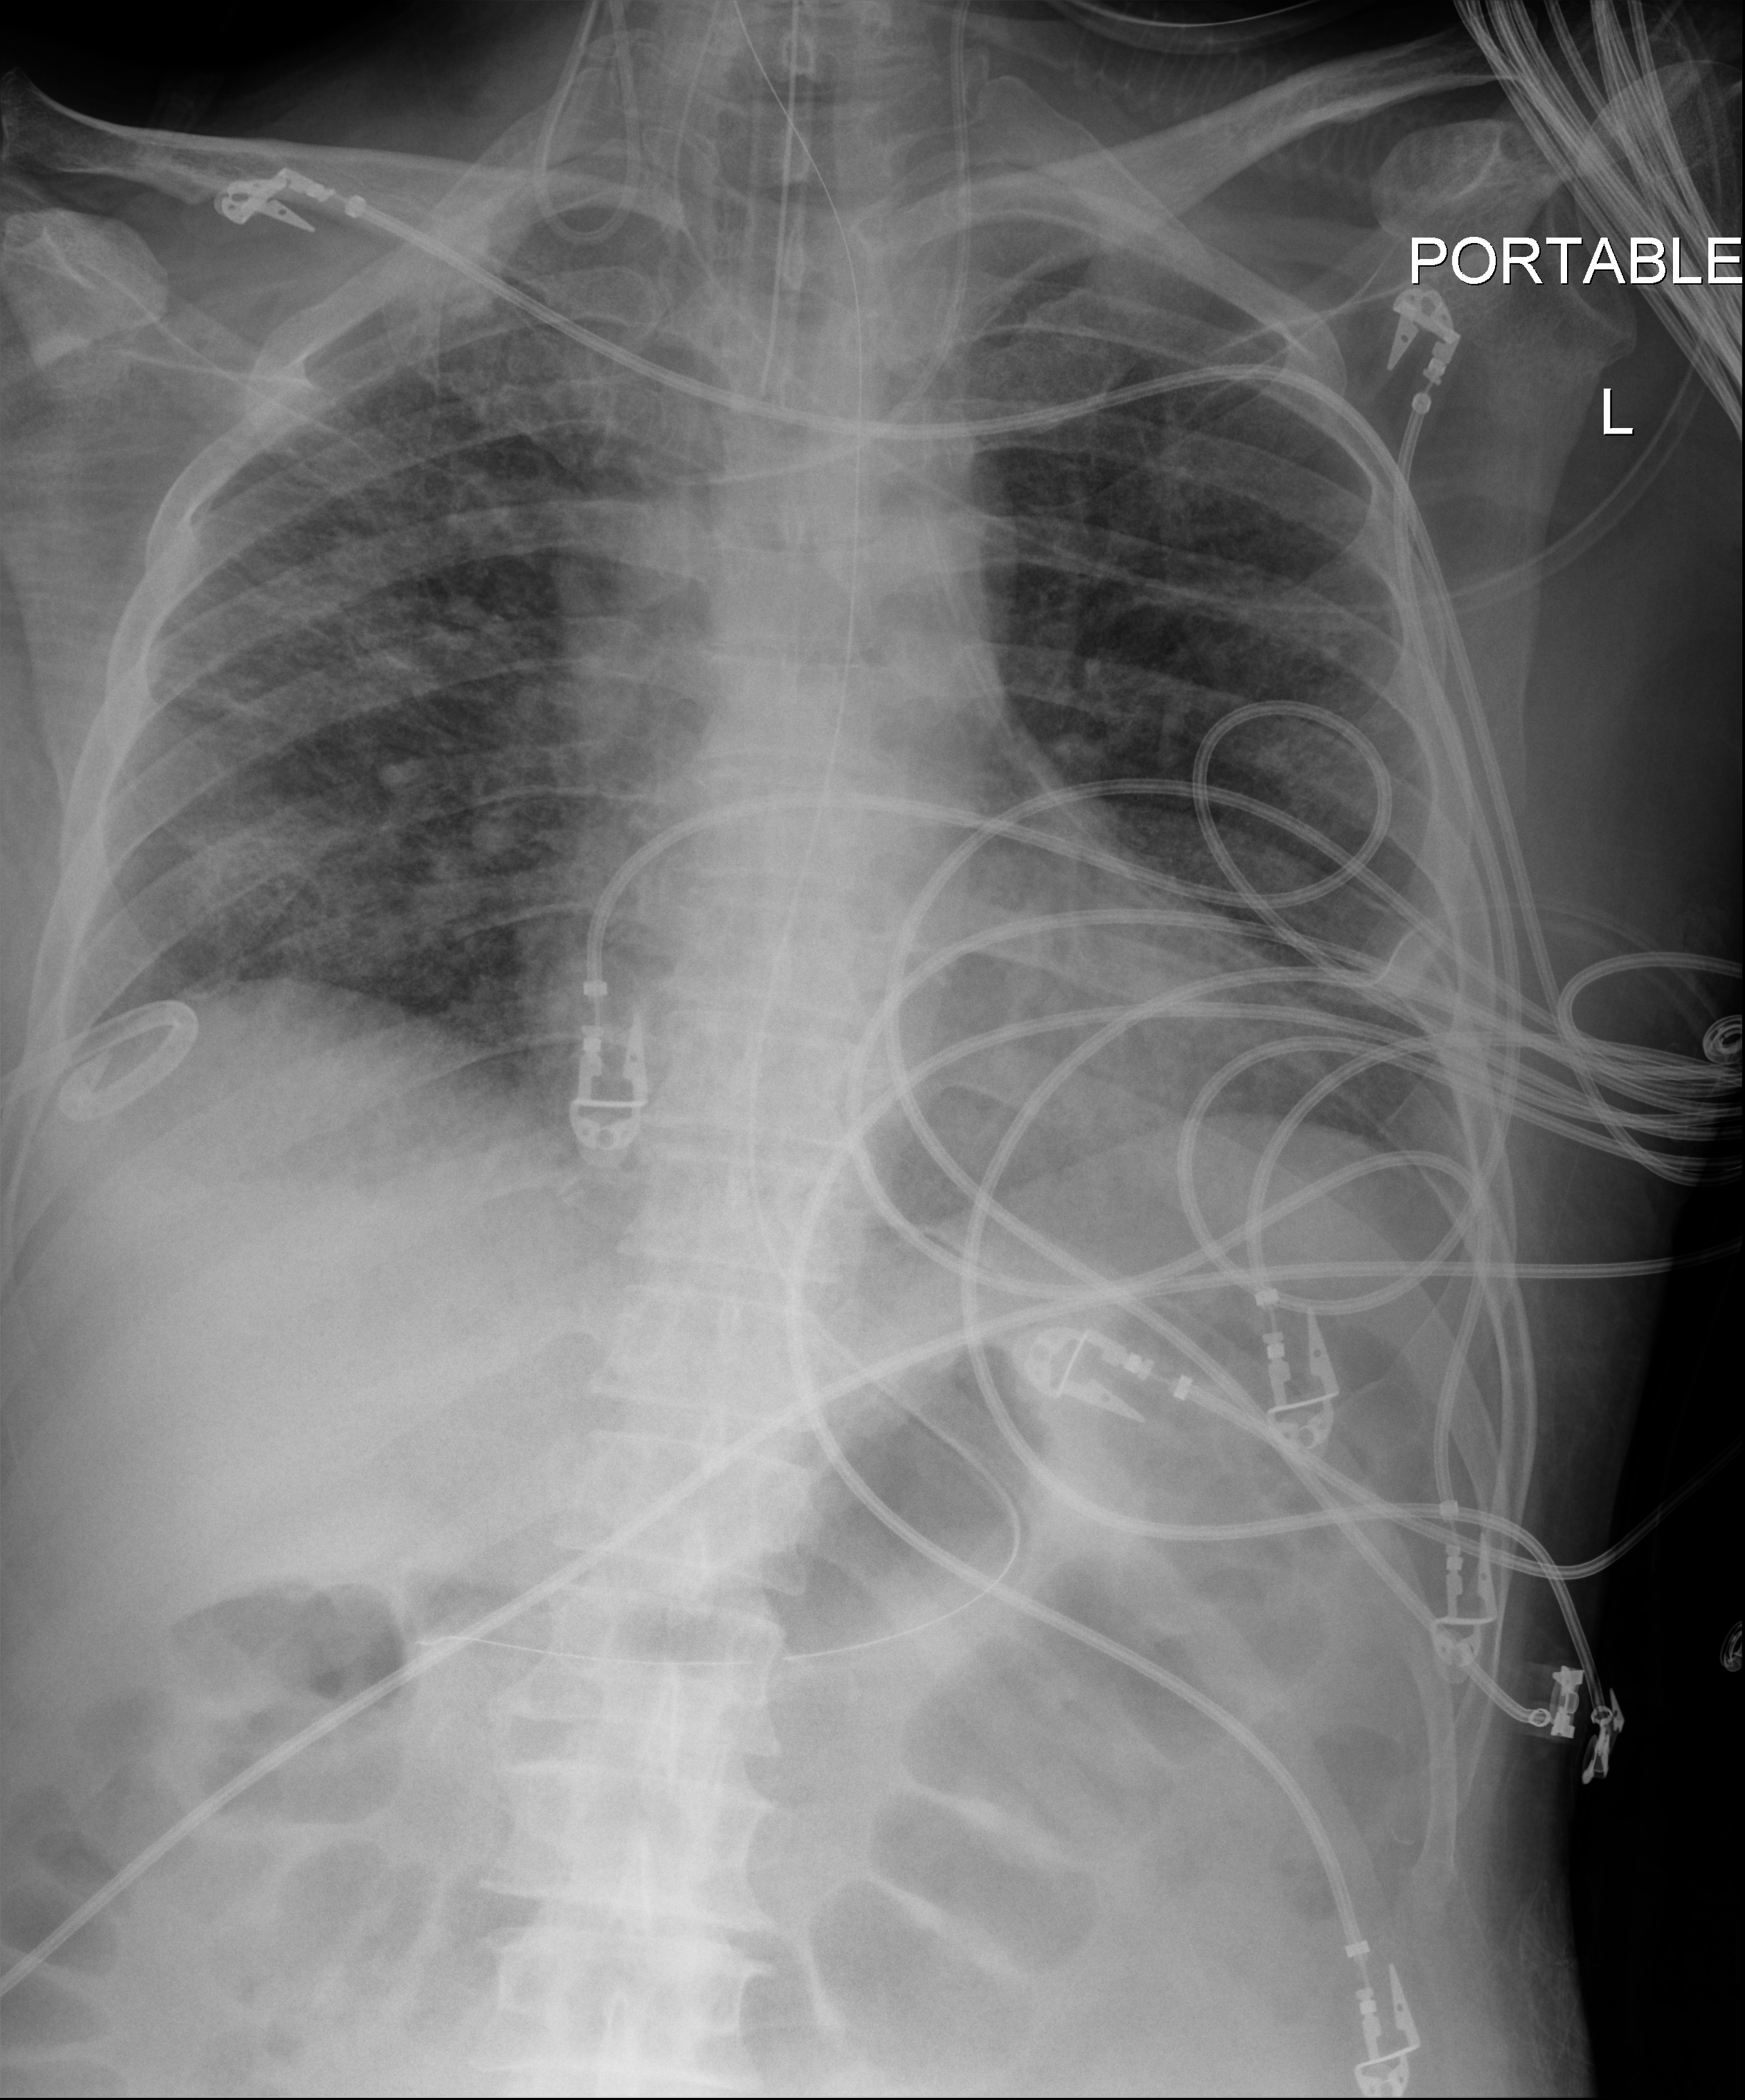
Bedside chest radiograph (digital radiography), anteroposterior (AP) projection. Male patient hospitalised with COVID-19, age 18–59 years.
Admission-level facts for this patient (not findings on this image; timing relative to this image not recorded): mechanically ventilated during this hospital stay: yes; COPD (admission record): no.